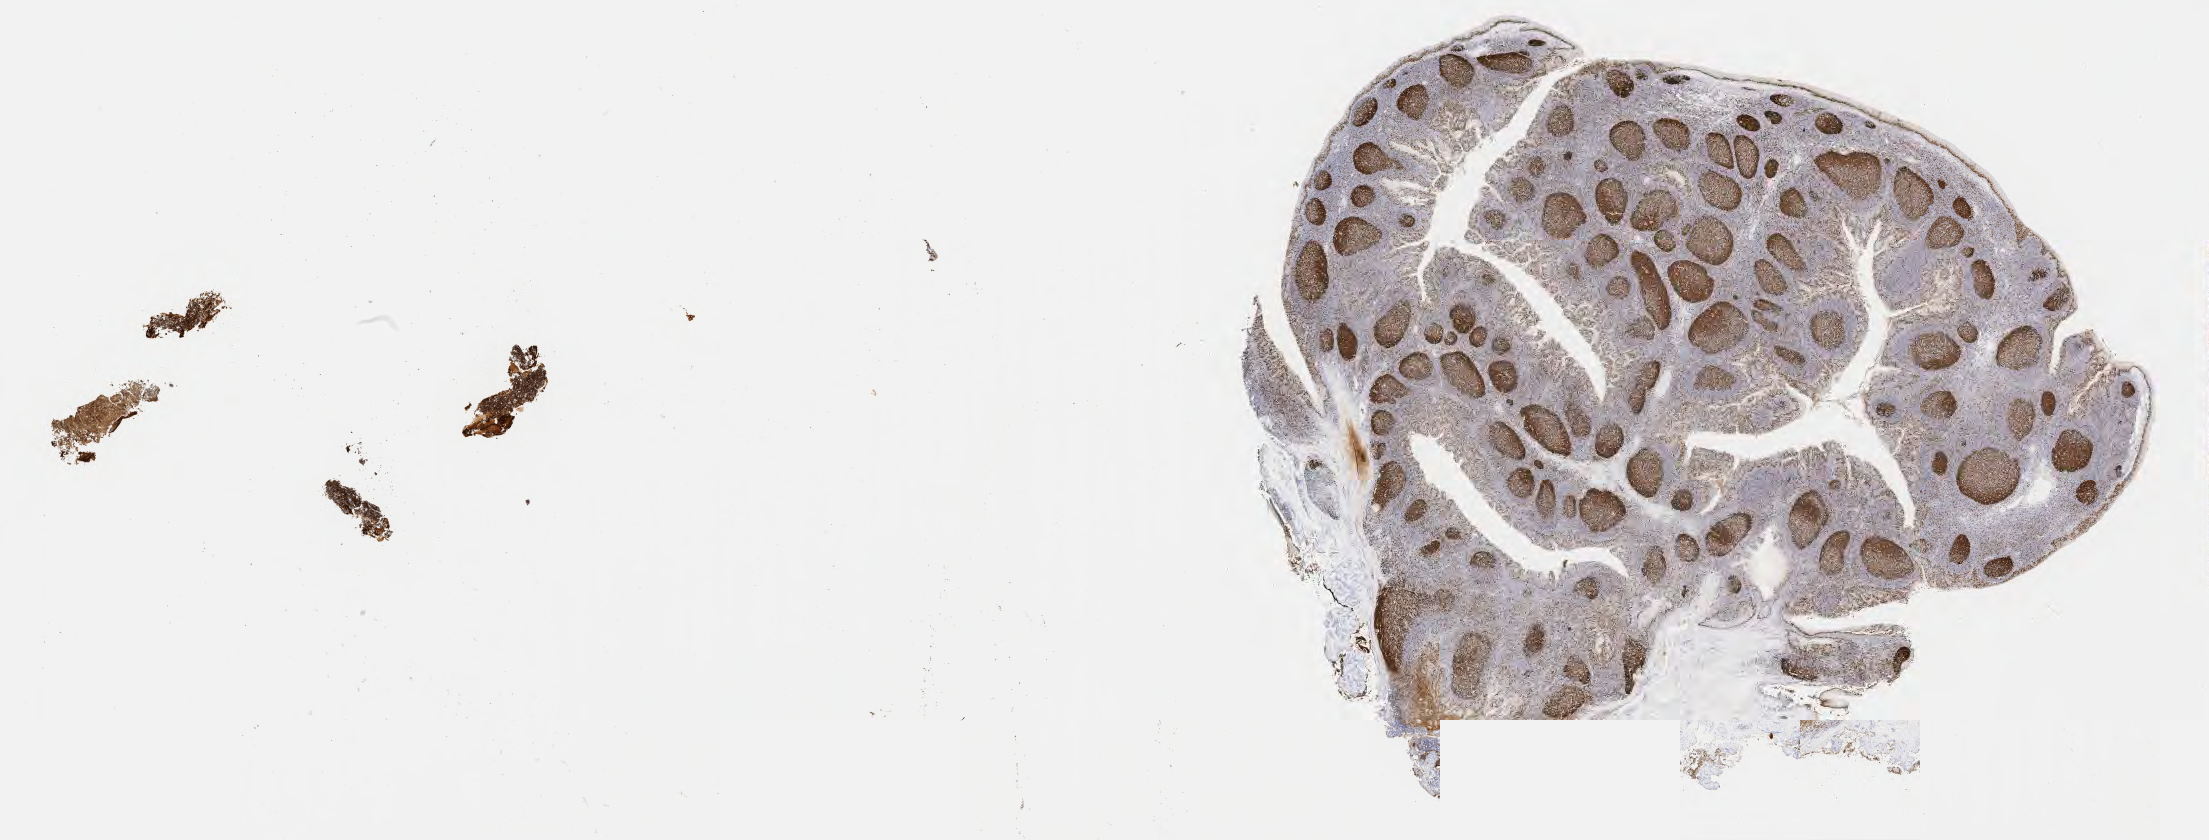
Immunohistochemistry (IHC) whole-slide image stained for Ki-67, low-resolution overview of the scanned area, about 35.7 x 13.6 mm; specimen: tumor tissue; site: lymph node of head and neck. Female patient; age at initial diagnosis 4 years.
- diagnosis: Burkitt lymphoma, NOS